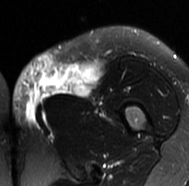
MRI of an extremity soft-tissue mass, one axial slice; slice 27 of 77 in the series (ordered by position); T2-weighted fat-saturated; MR volume resampled by the dataset authors to the PET/CT grid (not the native acquisition matrix); 3.27 mm slice thickness; 189 × 186 image matrix, field of view 185 × 182 mm. Female patient. Case-level facts recorded for this patient, not image findings: histological type: leiomyosarcoma; grade: high; site of the primary tumour: groin.
Structures marked on this image (expert contour drawn on MRI and transferred to this co-registered scan by the dataset authors):
- gross tumour volume including surrounding oedema: box from (x=12, y=52) to (x=100, y=130) px
- gross tumour volume (mass): (x=49, y=65)–(x=98, y=96)